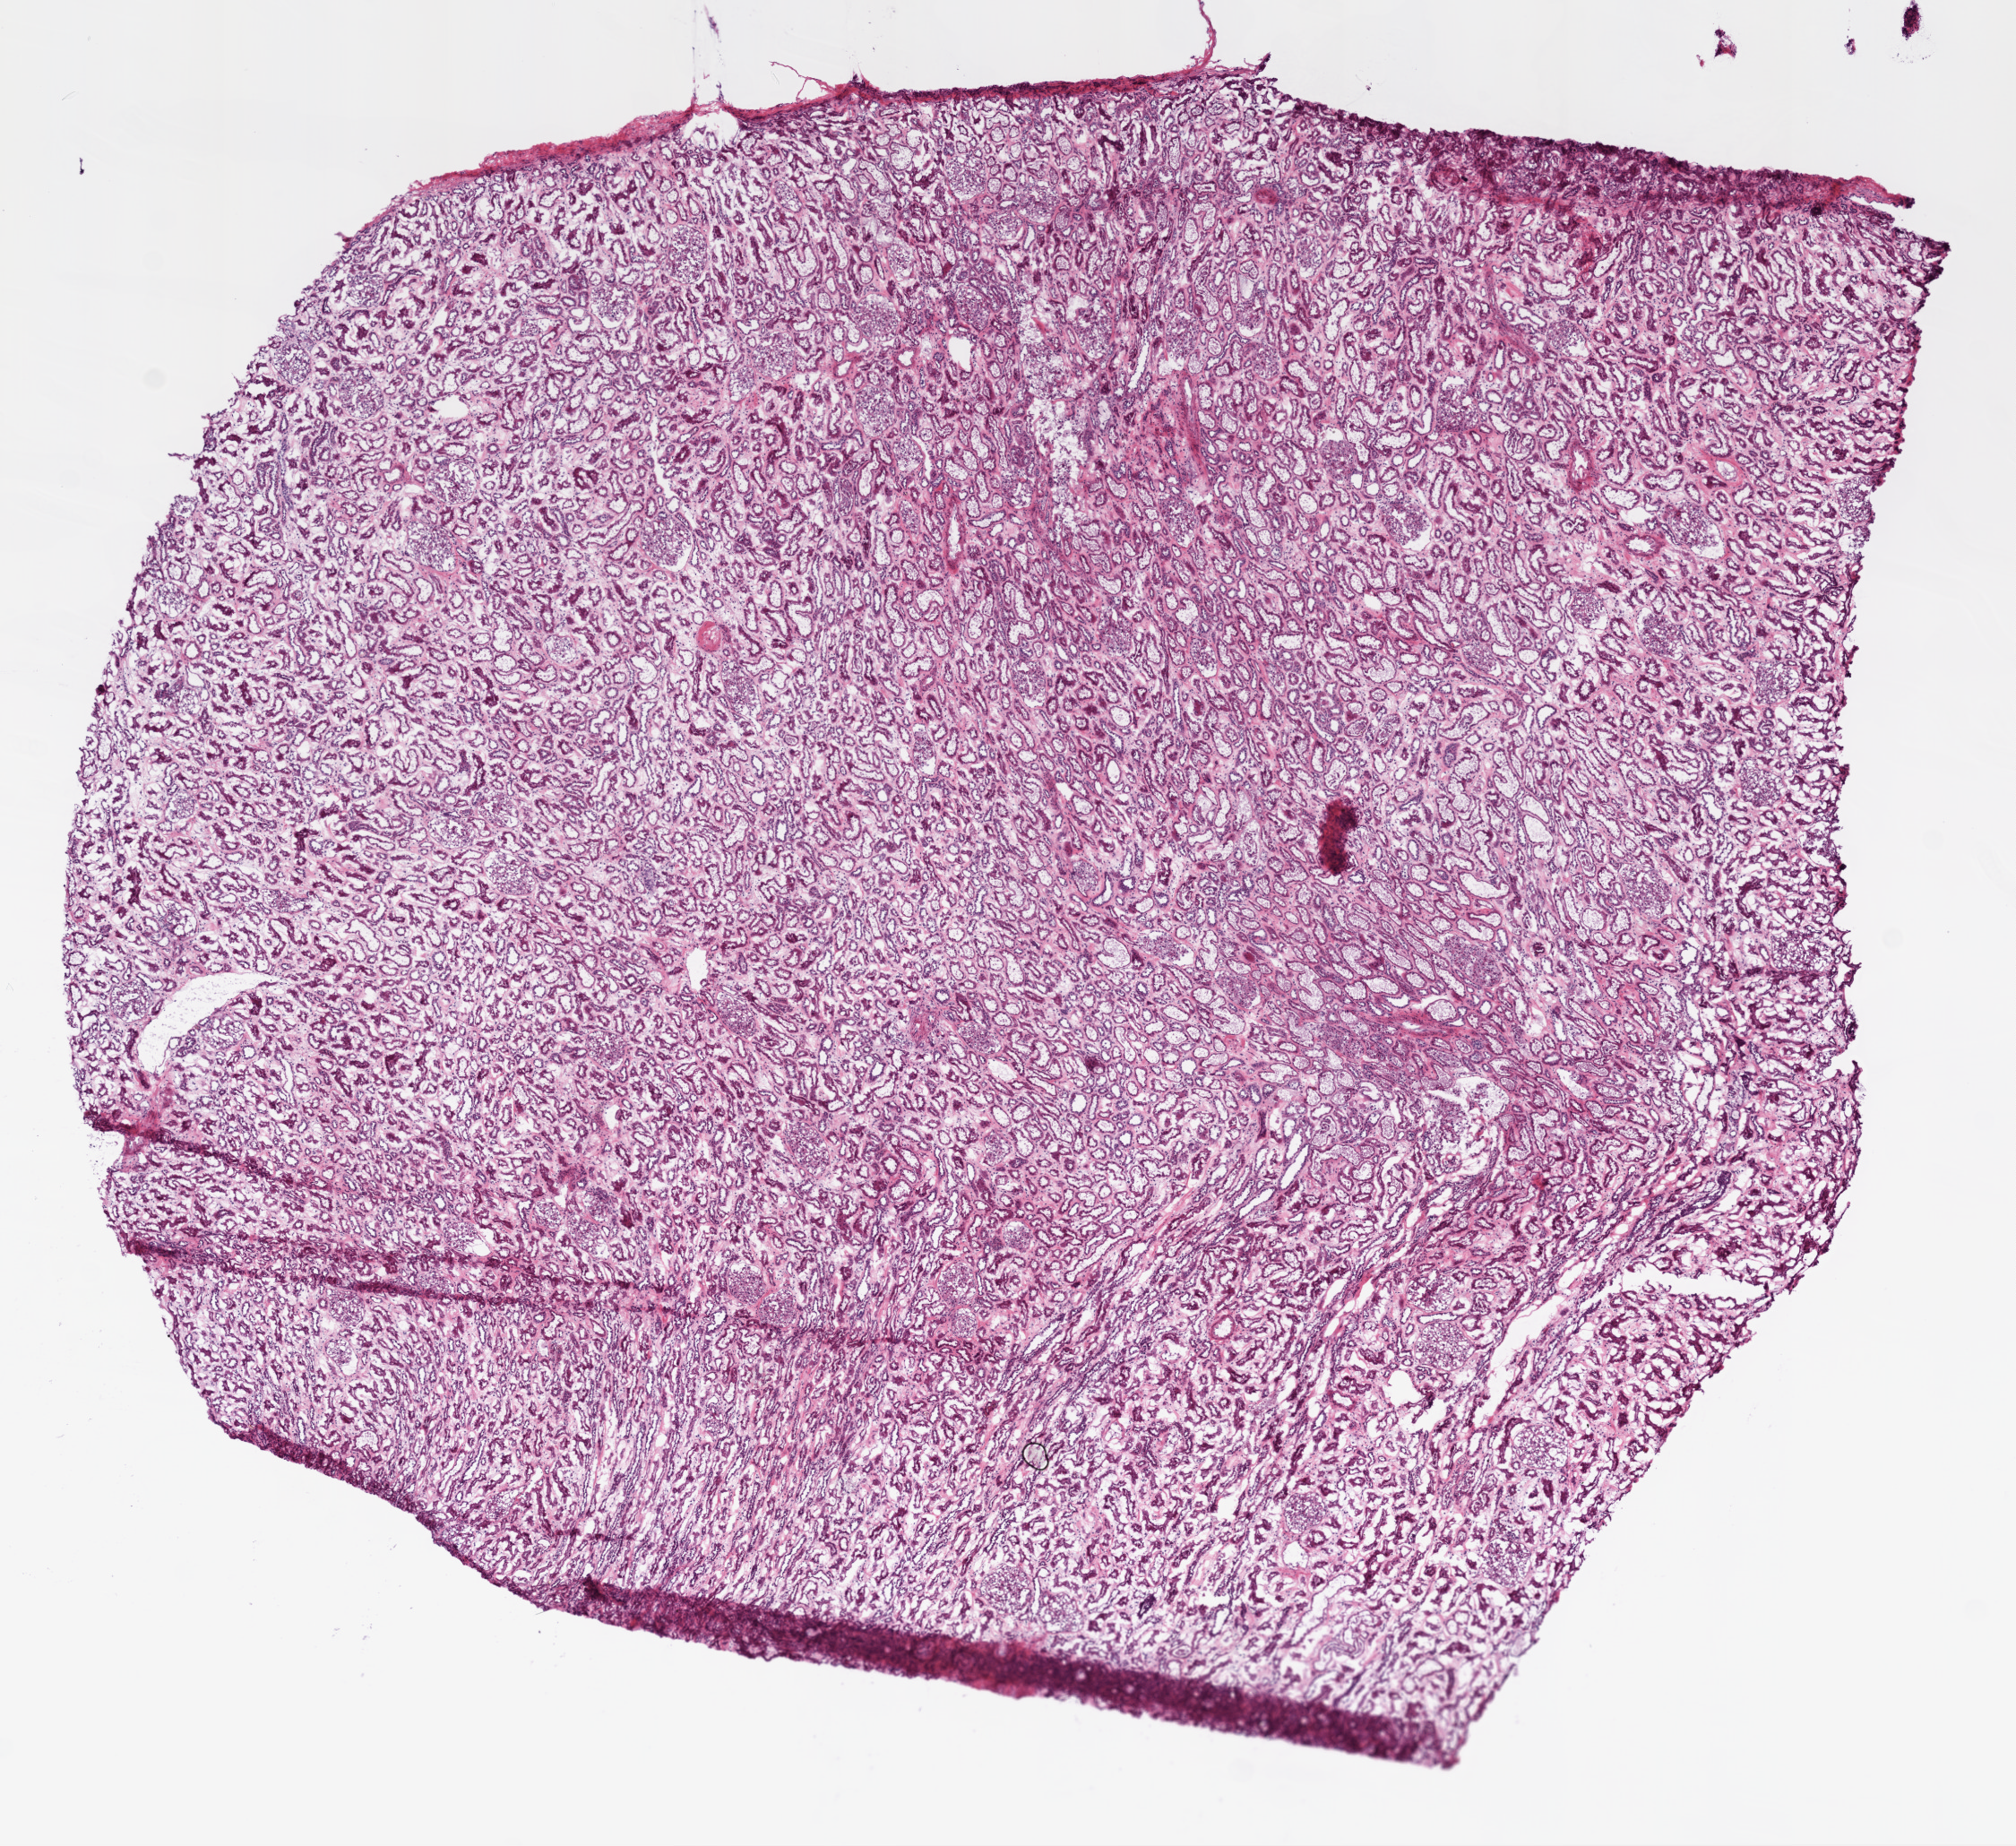
H&E whole-slide image — shown as a low-resolution overview of the whole scanned area (about 9.0 x 8.3 mm); frozen section from the top of the tissue portion; kidney, solid tissue normal (non-tumour tissue) sample. Female, age 60 years at initial diagnosis.
• this section: solid tissue normal sample (biorepository sample class)
• patient diagnosis: Clear cell adenocarcinoma, NOS